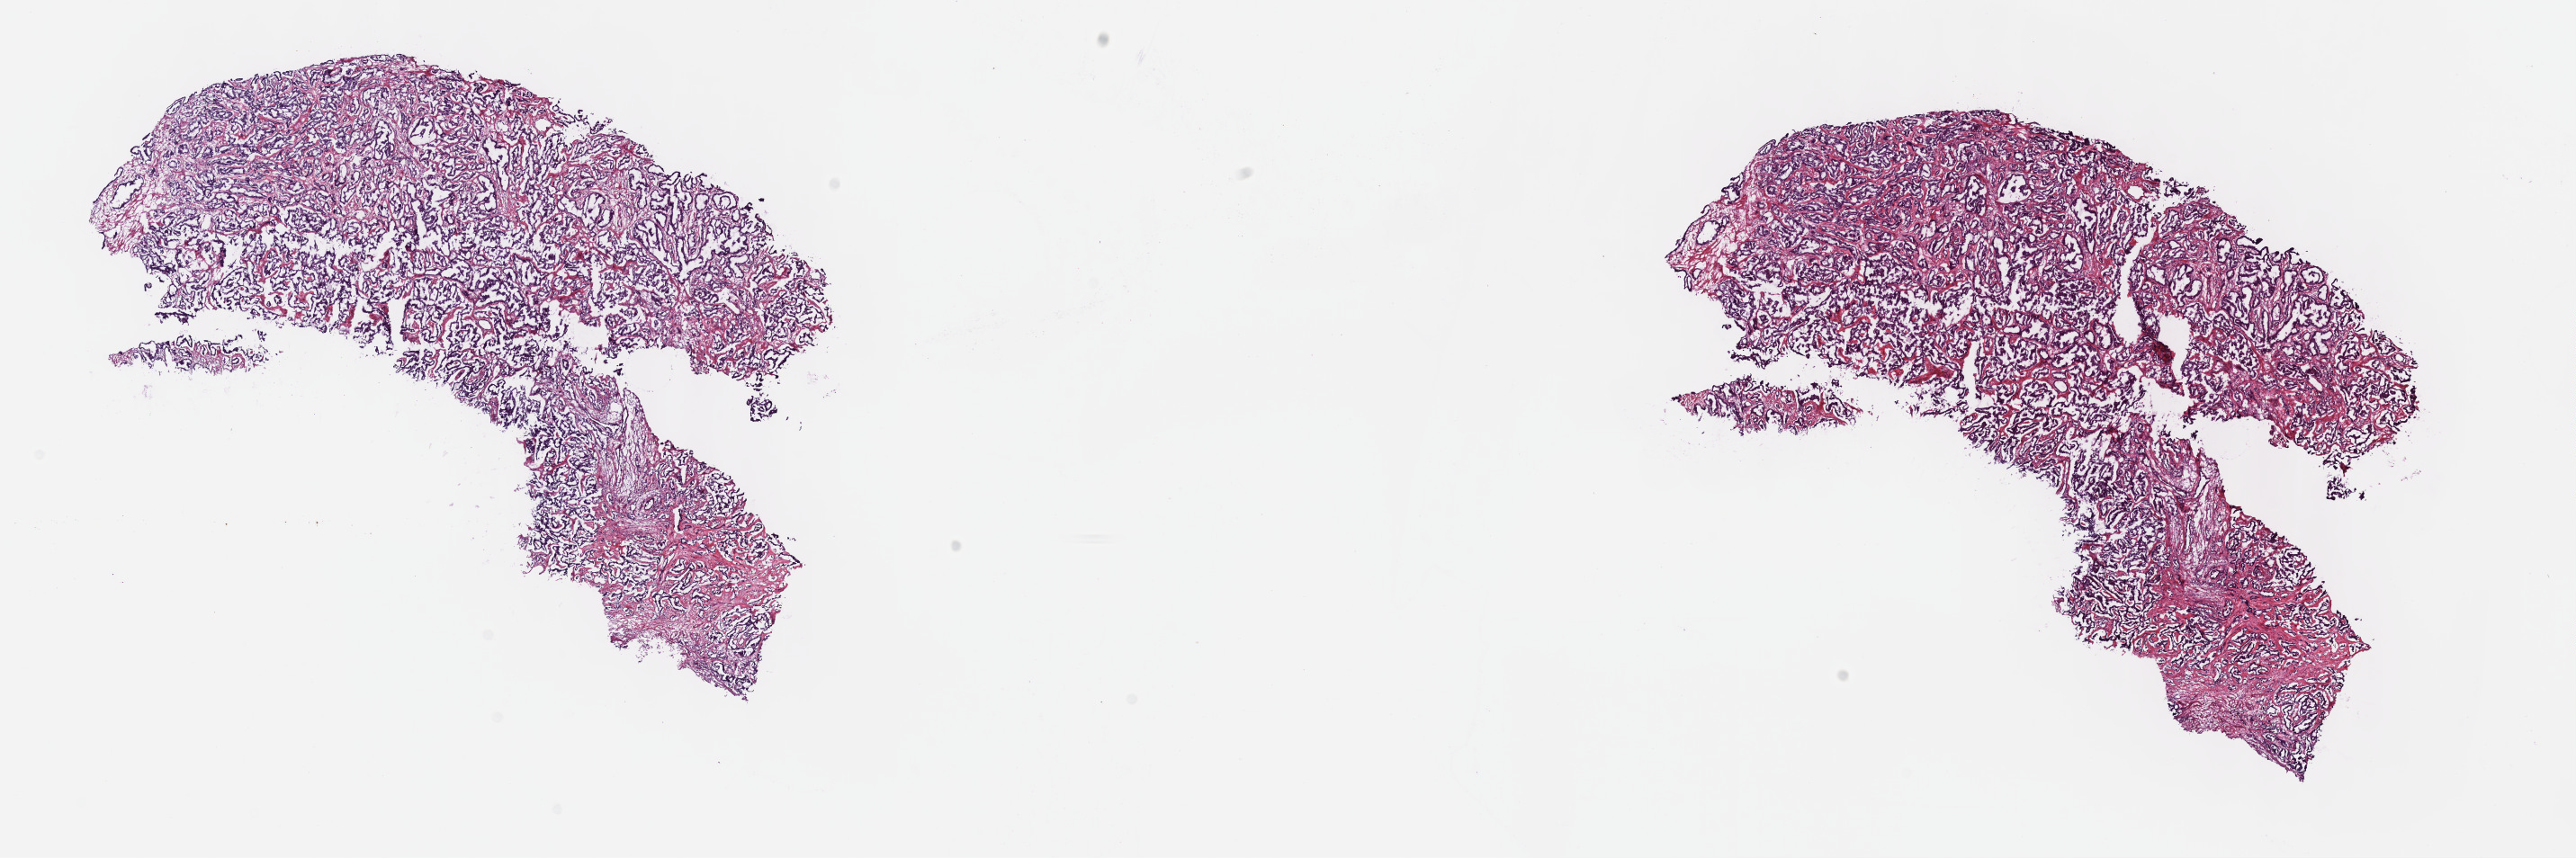
H&E whole-slide image — shown as a low-resolution overview of the whole scanned area (about 23.2 x 7.7 mm, slide scanned at 40x); frozen section from the top of the tissue portion; sample: primary tumour, prostate. Male, age 62 years at initial diagnosis. Gleason score: 7 (4+3). Slide review estimates, as recorded: tumour cells 80%, tumour nuclei 80%, normal cells 0%, stromal cells 20%, necrosis 0%. Infiltration values recorded for this section: lymphocyte infiltration 60%, monocyte infiltration 10%, neutrophil infiltration 20%.
• histologic diagnosis: Adenocarcinoma, NOS
• lymph nodes positive (case pathology): 0 of 50 examined